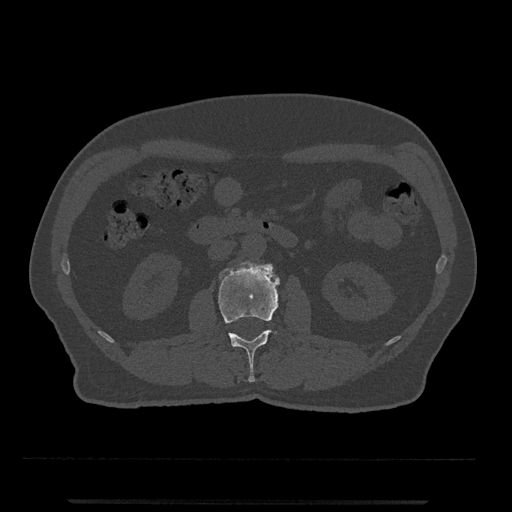
CT including the spine, one axial slice. Position 259 of 797 along the scan axis. Reconstruction kernel Br40s/3. 120 kVp. Bone window (W 1800 / L 400 HU). 512 × 512 image matrix, field of view 419 × 419 mm. Patient: male, 63 years. Case-level facts recorded for this patient, not image findings: primary cancer: prostate.
Annotated regions visible in this slice (semi-automatically segmented with operator editing):
- L2 vertebra: bounding box <218,261,280,382> (left, top, right, bottom; pixels)